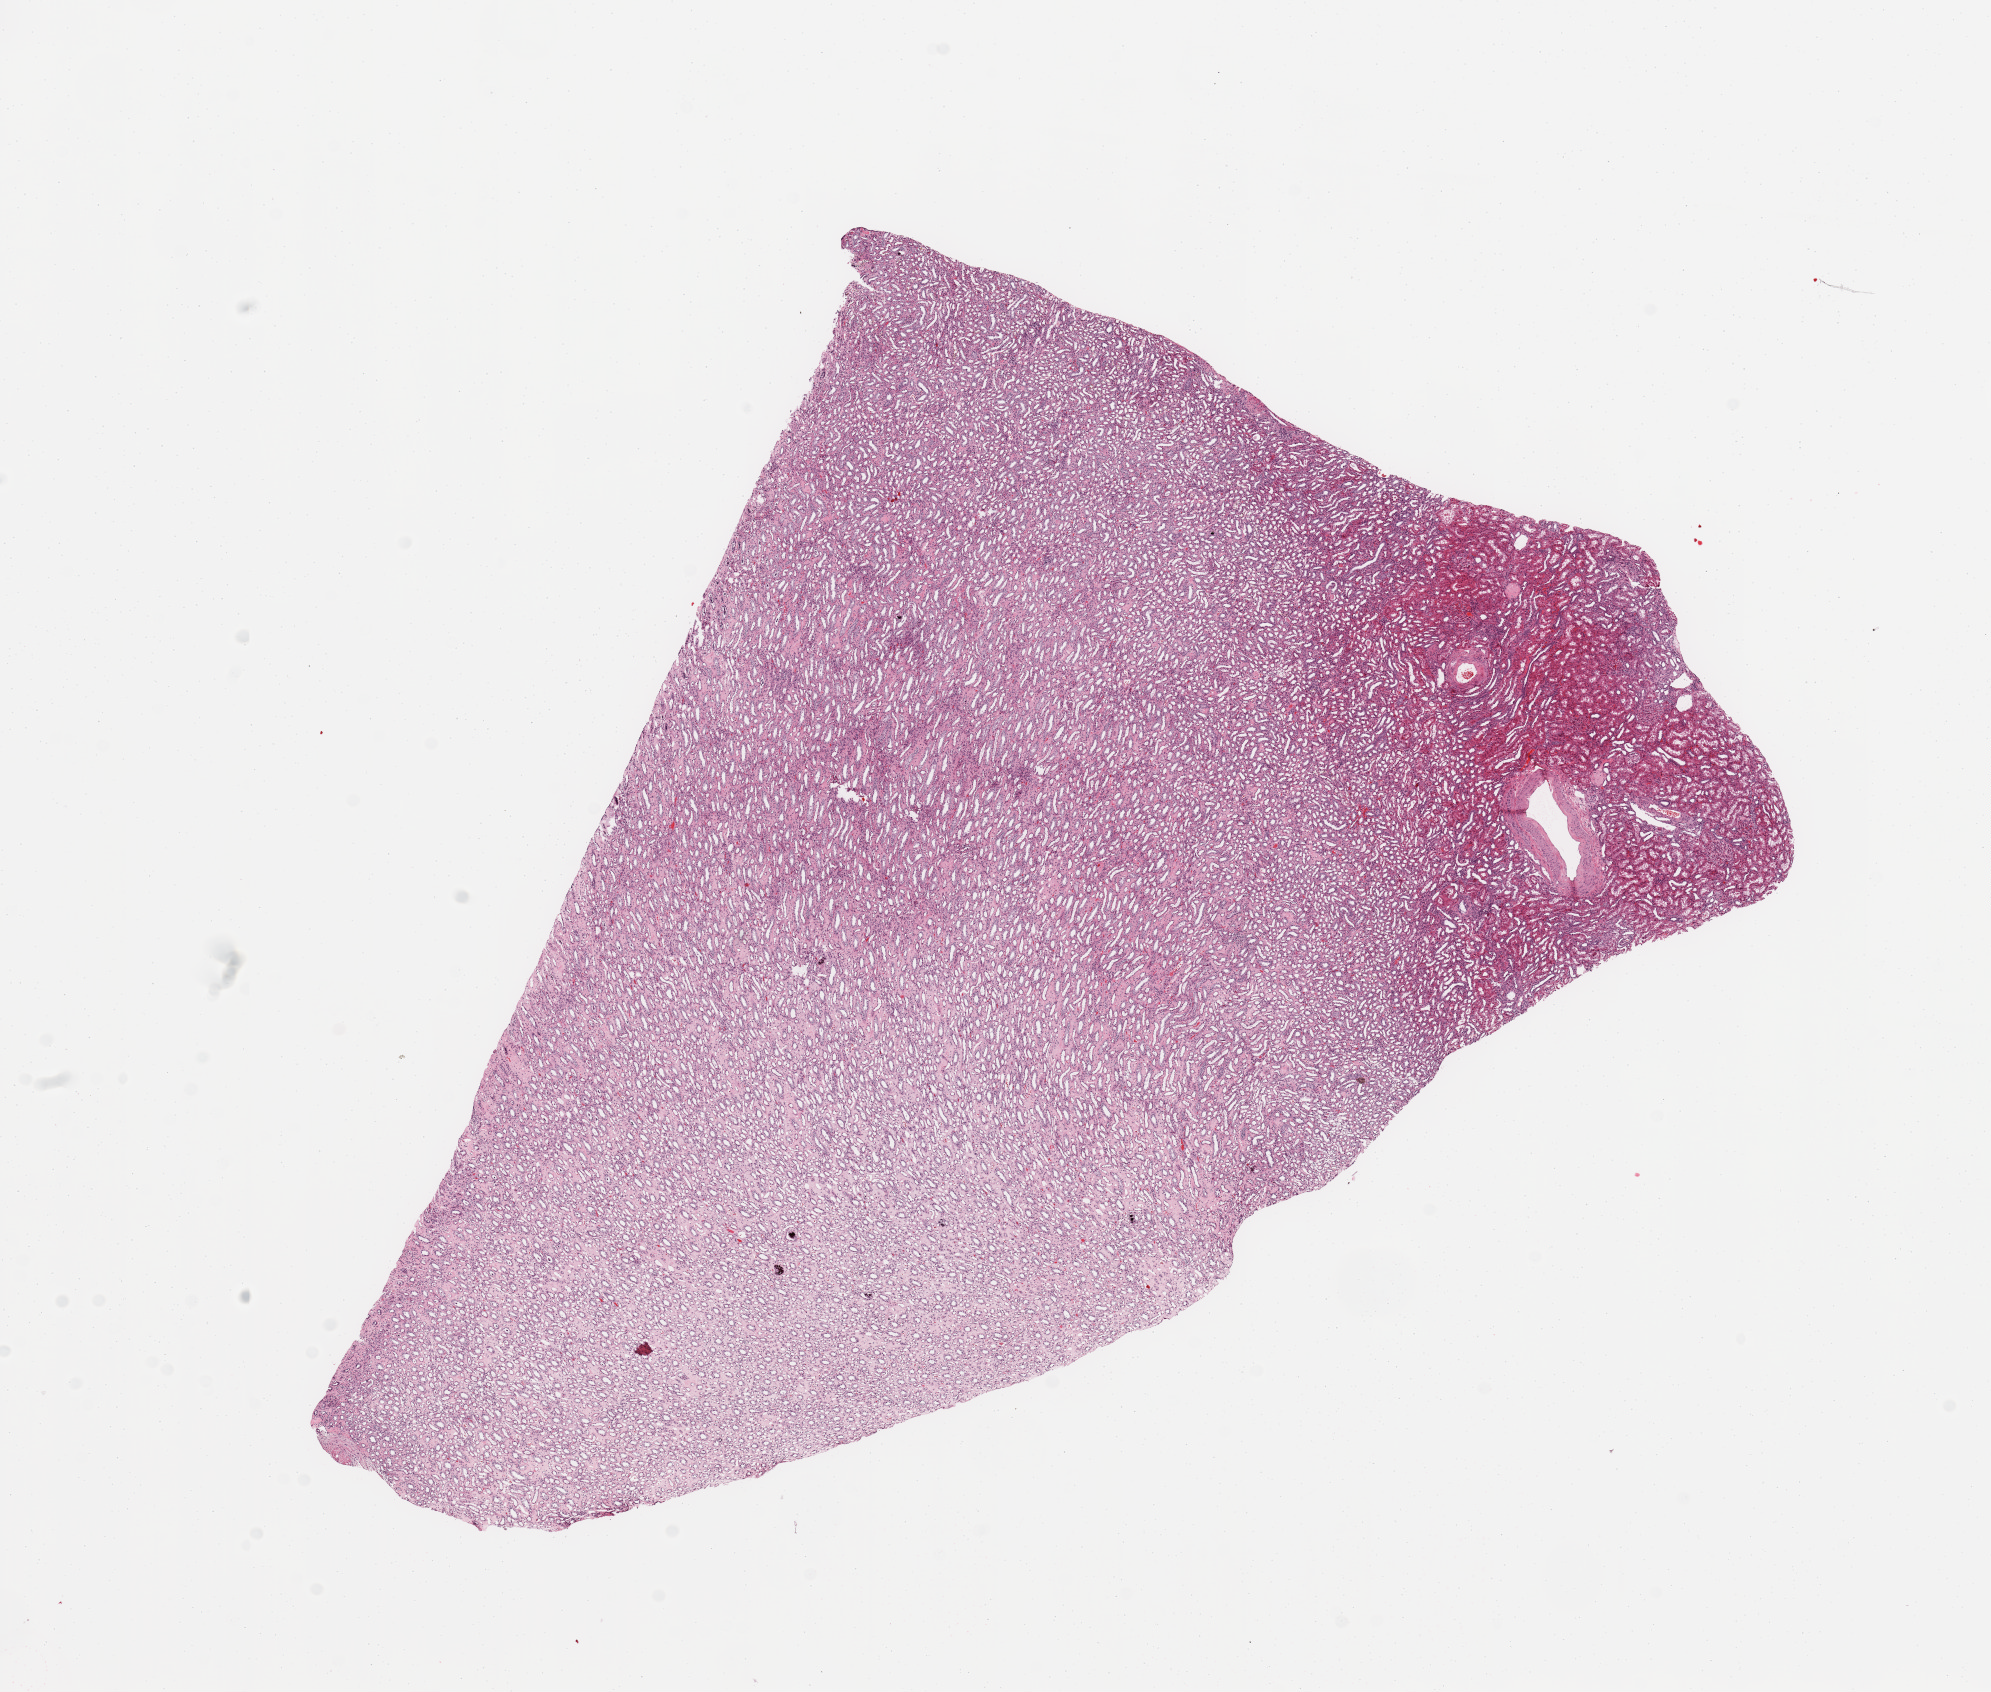
Whole-slide histology image, Hematoxylin and eosin (H&E) stained, low-resolution overview of the scanned area, about 15.8 x 13.4 mm; normal (non-tumour) tissue sample, sampled site: kidney. Patient: female, age 57 years.
This section: normal (non-tumour) tissue from the same patient. Patient diagnosis: Renal cell carcinoma, NOS.